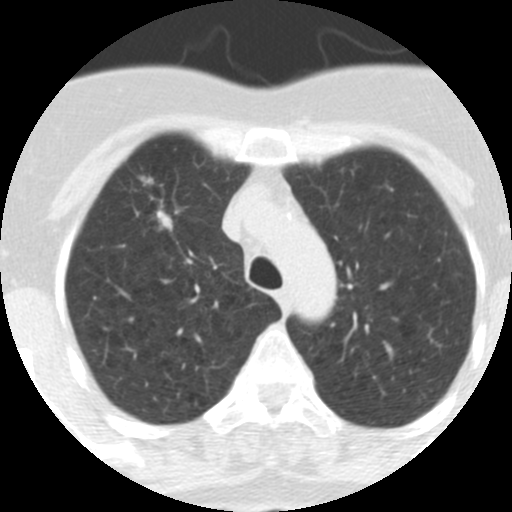
Low-dose screening chest CT, one axial slice; position 244 of 313 along the scan axis; lung window (W 1500 / L -600 HU); 2.5 mm slice thickness; 512 × 512 image matrix.
Annotated regions visible in this slice (expert manual segmentation):
- lesion 1 (tumor, upper lobe of right lung): box from (x=157, y=210) to (x=173, y=231) px